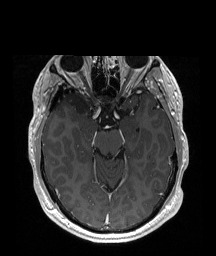
Brain MRI from a brain-tumour surgery series, one axial slice; position 122 of 192 along the scan axis; T1-weighted post-contrast; 1 mm slice thickness; 216 × 256 image matrix, field of view 219 × 260 mm. Case-level facts recorded for this patient, not image findings: histopathology: Astrocytoma; WHO grade: 2; IDH mutation: yes.
Annotated regions visible in this slice (expert manual segmentation):
- tumour: bounding box (x1, y1, x2, y2) in pixels: (69, 92, 90, 122)